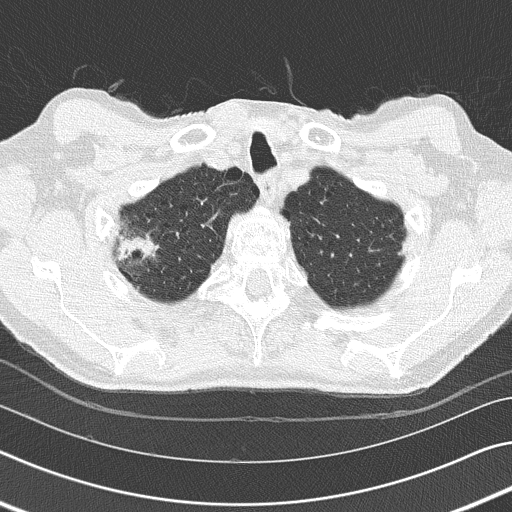
Low-dose screening chest CT, one axial slice. Position 142 of 155 along the scan axis. 120 kVp. Lung window (W 1500 / L -600 HU). 2 mm slice thickness. 512 × 512 image matrix, field of view 340 × 340 mm.
Structures marked on this image (manually delineated by an expert):
- lesion 1 (tumor, middle lobe of right lung): box from (x=117, y=231) to (x=160, y=263) px